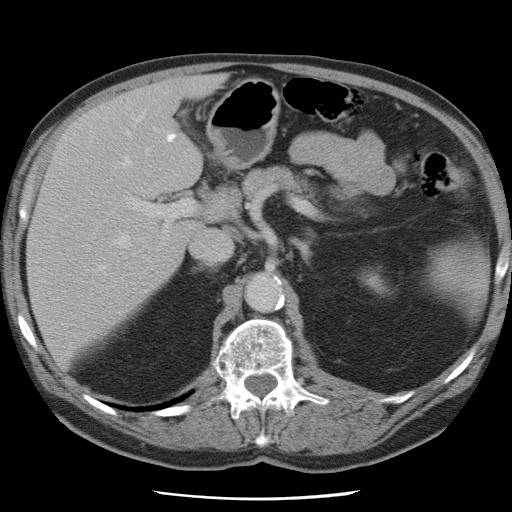
Contrast-enhanced abdominal CT, one axial slice; 120 kVp; intravenous contrast given; soft-tissue window (W 400 / L 40 HU); 512 × 512 image matrix, field of view 337 × 337 mm. Male patient, age 75 years. Case-level facts recorded for this patient, not image findings: diagnosis: colorectal cancer liver metastases, imaged before liver resection; multiple liver metastases: yes; largest metastasis: 2.4 cm; disease in both lobes: yes.
Outlined on this slice (manually delineated by an expert):
- hepatic veins: bounding box (x1, y1, x2, y2) in pixels: (81, 114, 149, 282)
- liver: (28, 78, 219, 362)
- planned liver remnant (the part of the liver to remain after resection): (28, 121, 190, 363)
- portal vein (with intrahepatic branches): (126, 133, 199, 233)